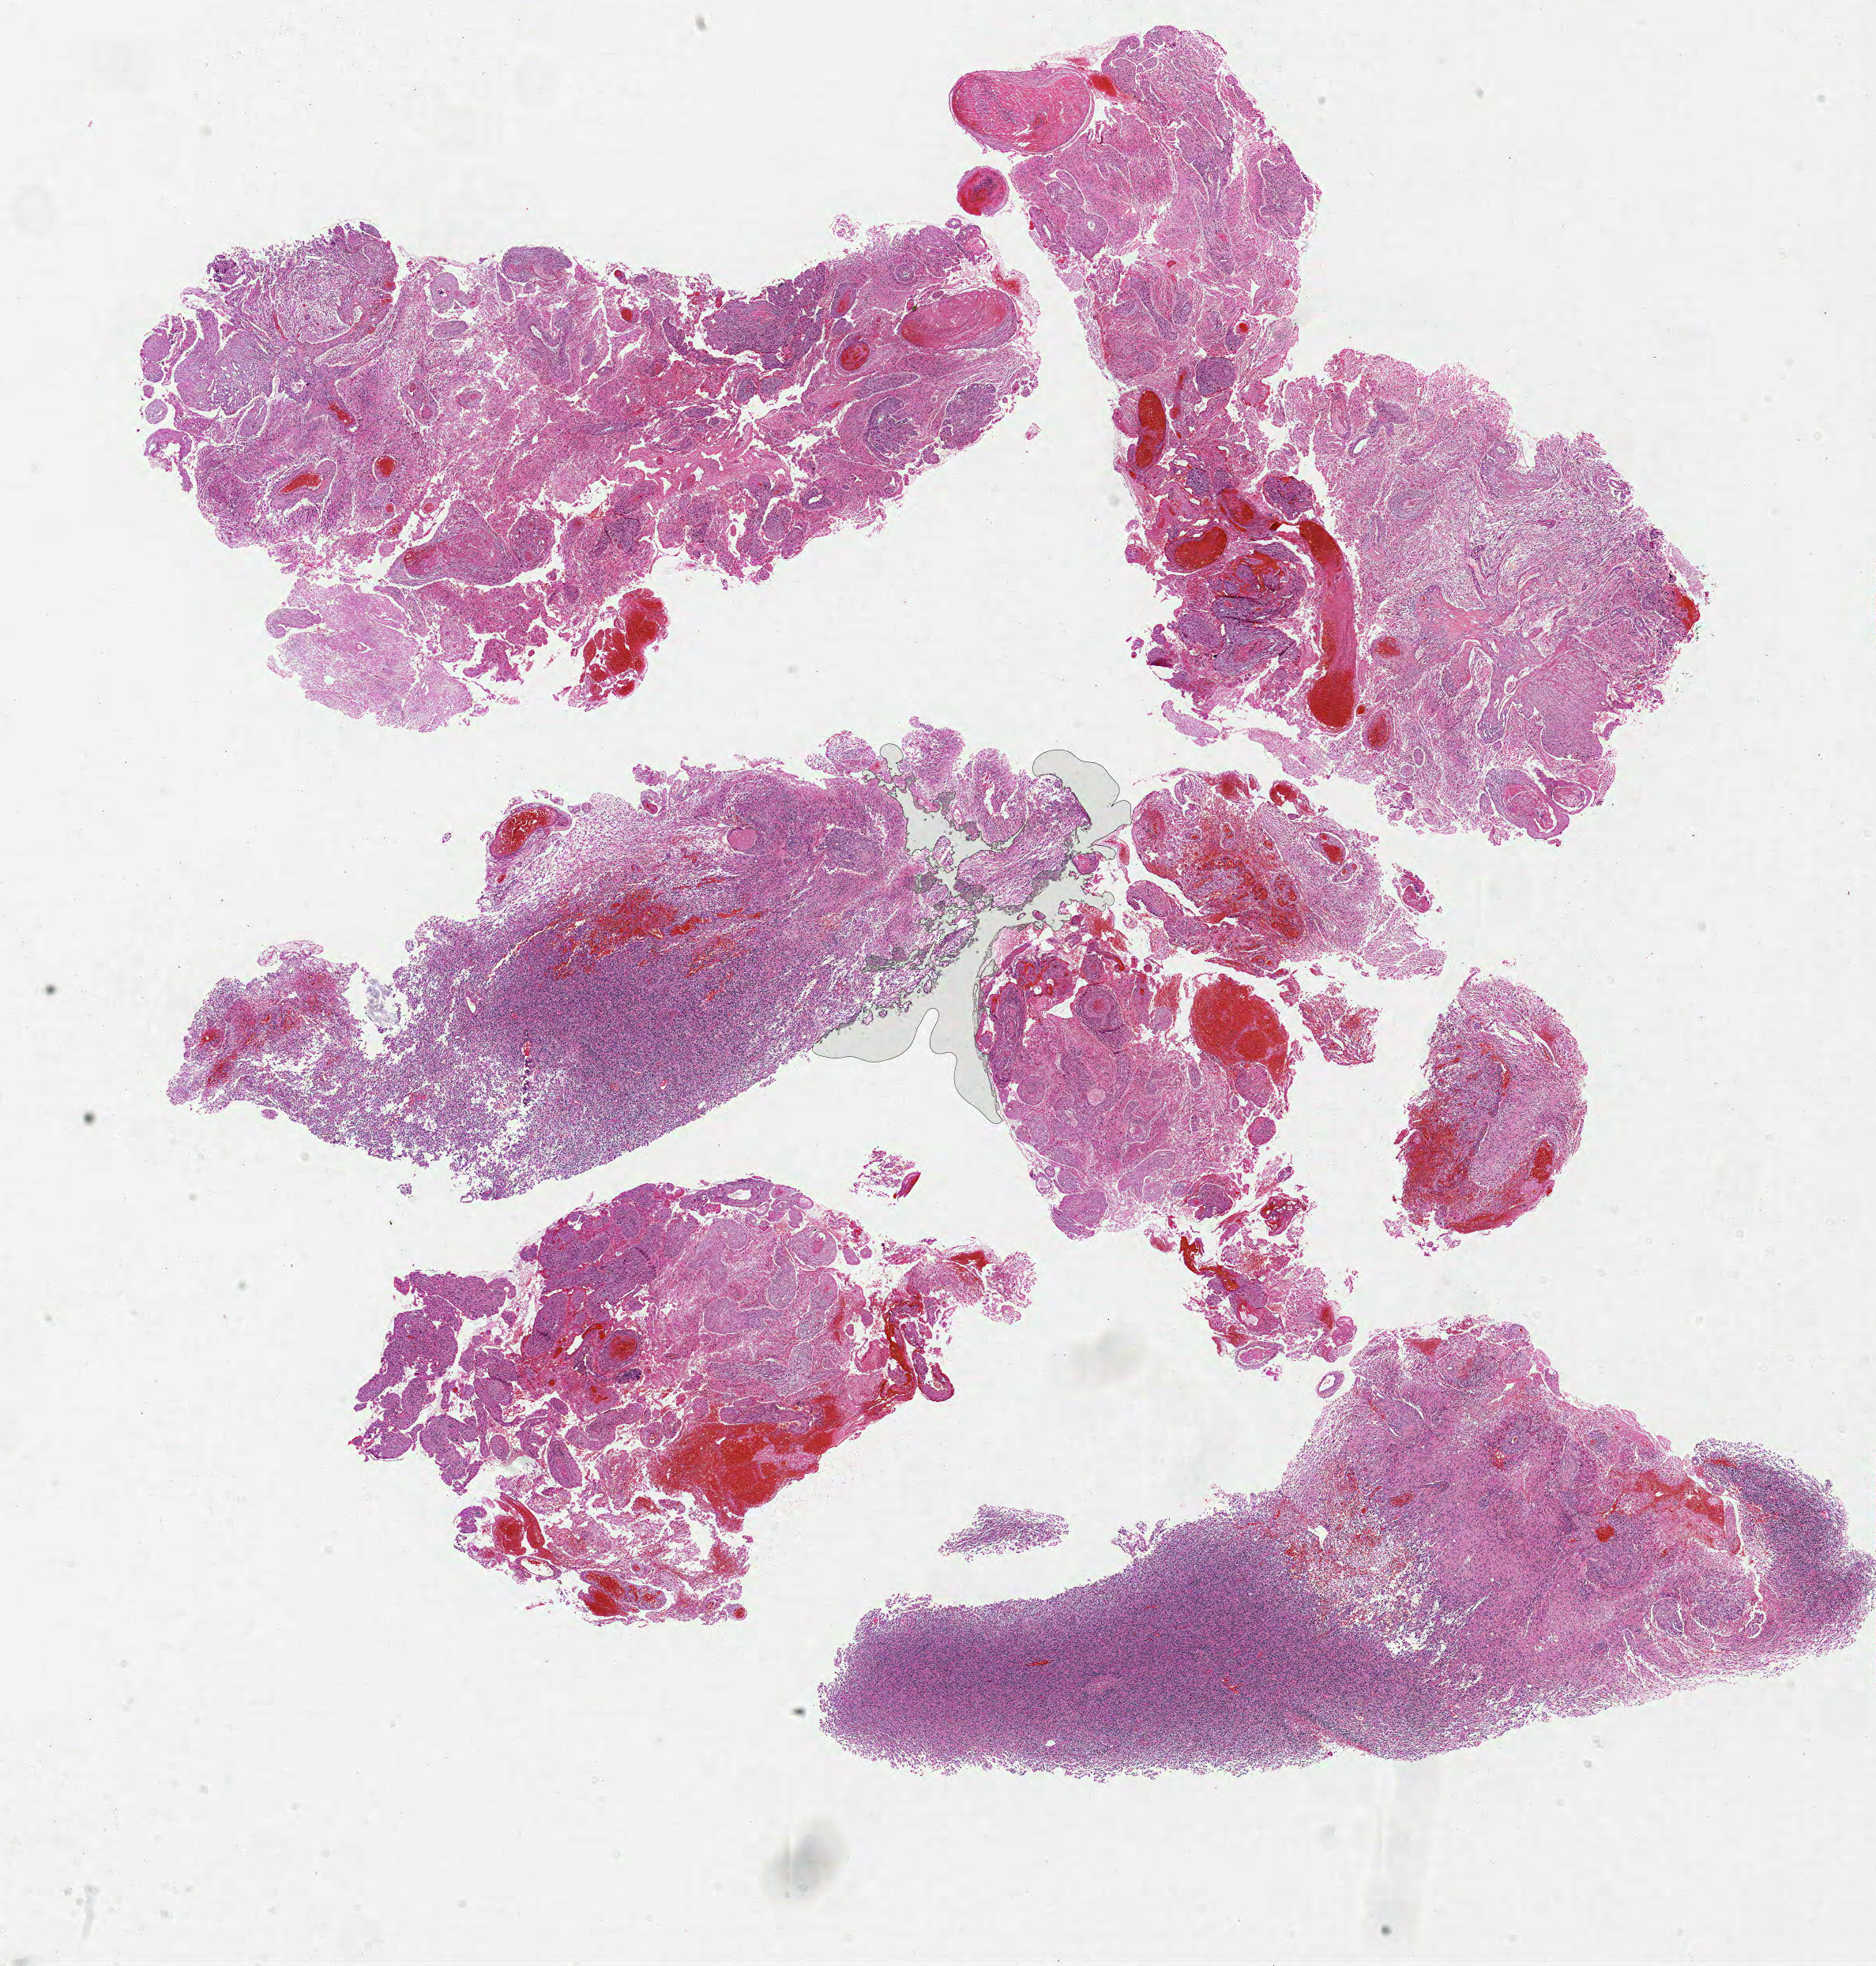
H&E-stained whole-slide image, low-resolution overview of the scanned area, about 19.0 x 19.9 mm (from a 20x scan). Formalin-fixed paraffin-embedded (FFPE) diagnostic section. Primary tumour sample from the brain. Female patient; age at initial diagnosis 75 years.
* histologic diagnosis: Glioblastoma